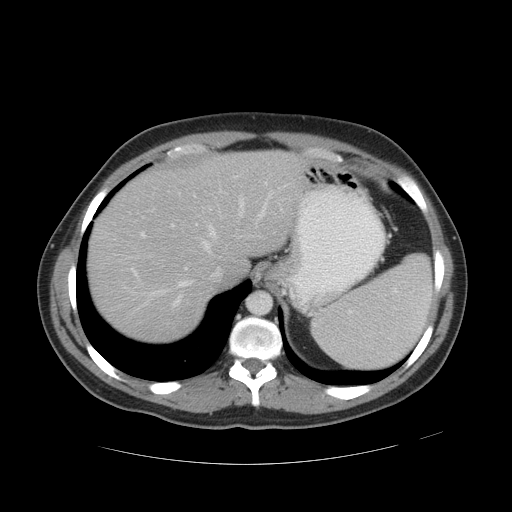
Contrast-enhanced abdominal CT, one axial slice; position 40 of 49 along the scan axis; reconstruction kernel STANDARD; 120 kVp; intravenous contrast given; soft-tissue window (W 400 / L 40 HU); 5 mm slice thickness; 512 × 512 image matrix, field of view 422 × 422 mm. Male patient, age 42 years. From the clinical record (not read from this slice): diagnosis: colorectal cancer liver metastases, imaged before liver resection; multiple liver metastases: yes; largest metastasis: 2.8 cm; disease in both lobes: yes.
Structures marked on this image (outlined manually by an expert reader):
- hepatic veins: bounding box [x1, y1, x2, y2] px = [128, 185, 268, 314]
- liver: [89, 153, 300, 341]
- planned liver remnant (the part of the liver to remain after resection): [89, 152, 300, 341]
- portal vein (with intrahepatic branches): [131, 176, 268, 276]